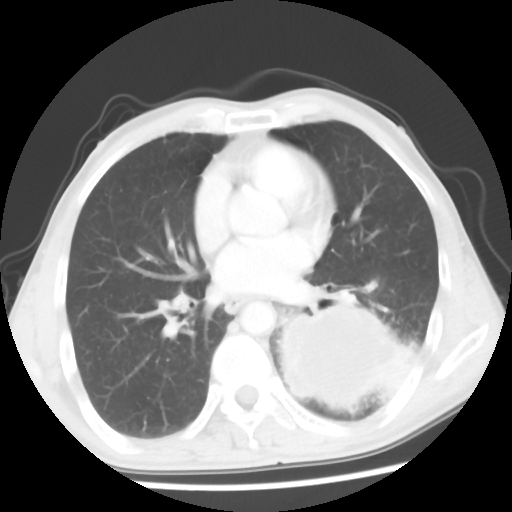
Chest CT, one axial slice; slice 27 of 56 in the series (ordered by position); lung window (W 1500 / L -600 HU); 5 mm slice thickness; 512 × 512 image matrix, field of view 318 × 318 mm. Male patient, age 60 years. Case-level facts recorded for this patient, not image findings: clinical TNM (as recorded): T4 N0 M0.
Structures marked on this image (bounding box drawn by a radiologist):
- lung tumour (recorded histology: squamous cell carcinoma): bounding box [x1, y1, x2, y2] px = [274, 296, 401, 410]